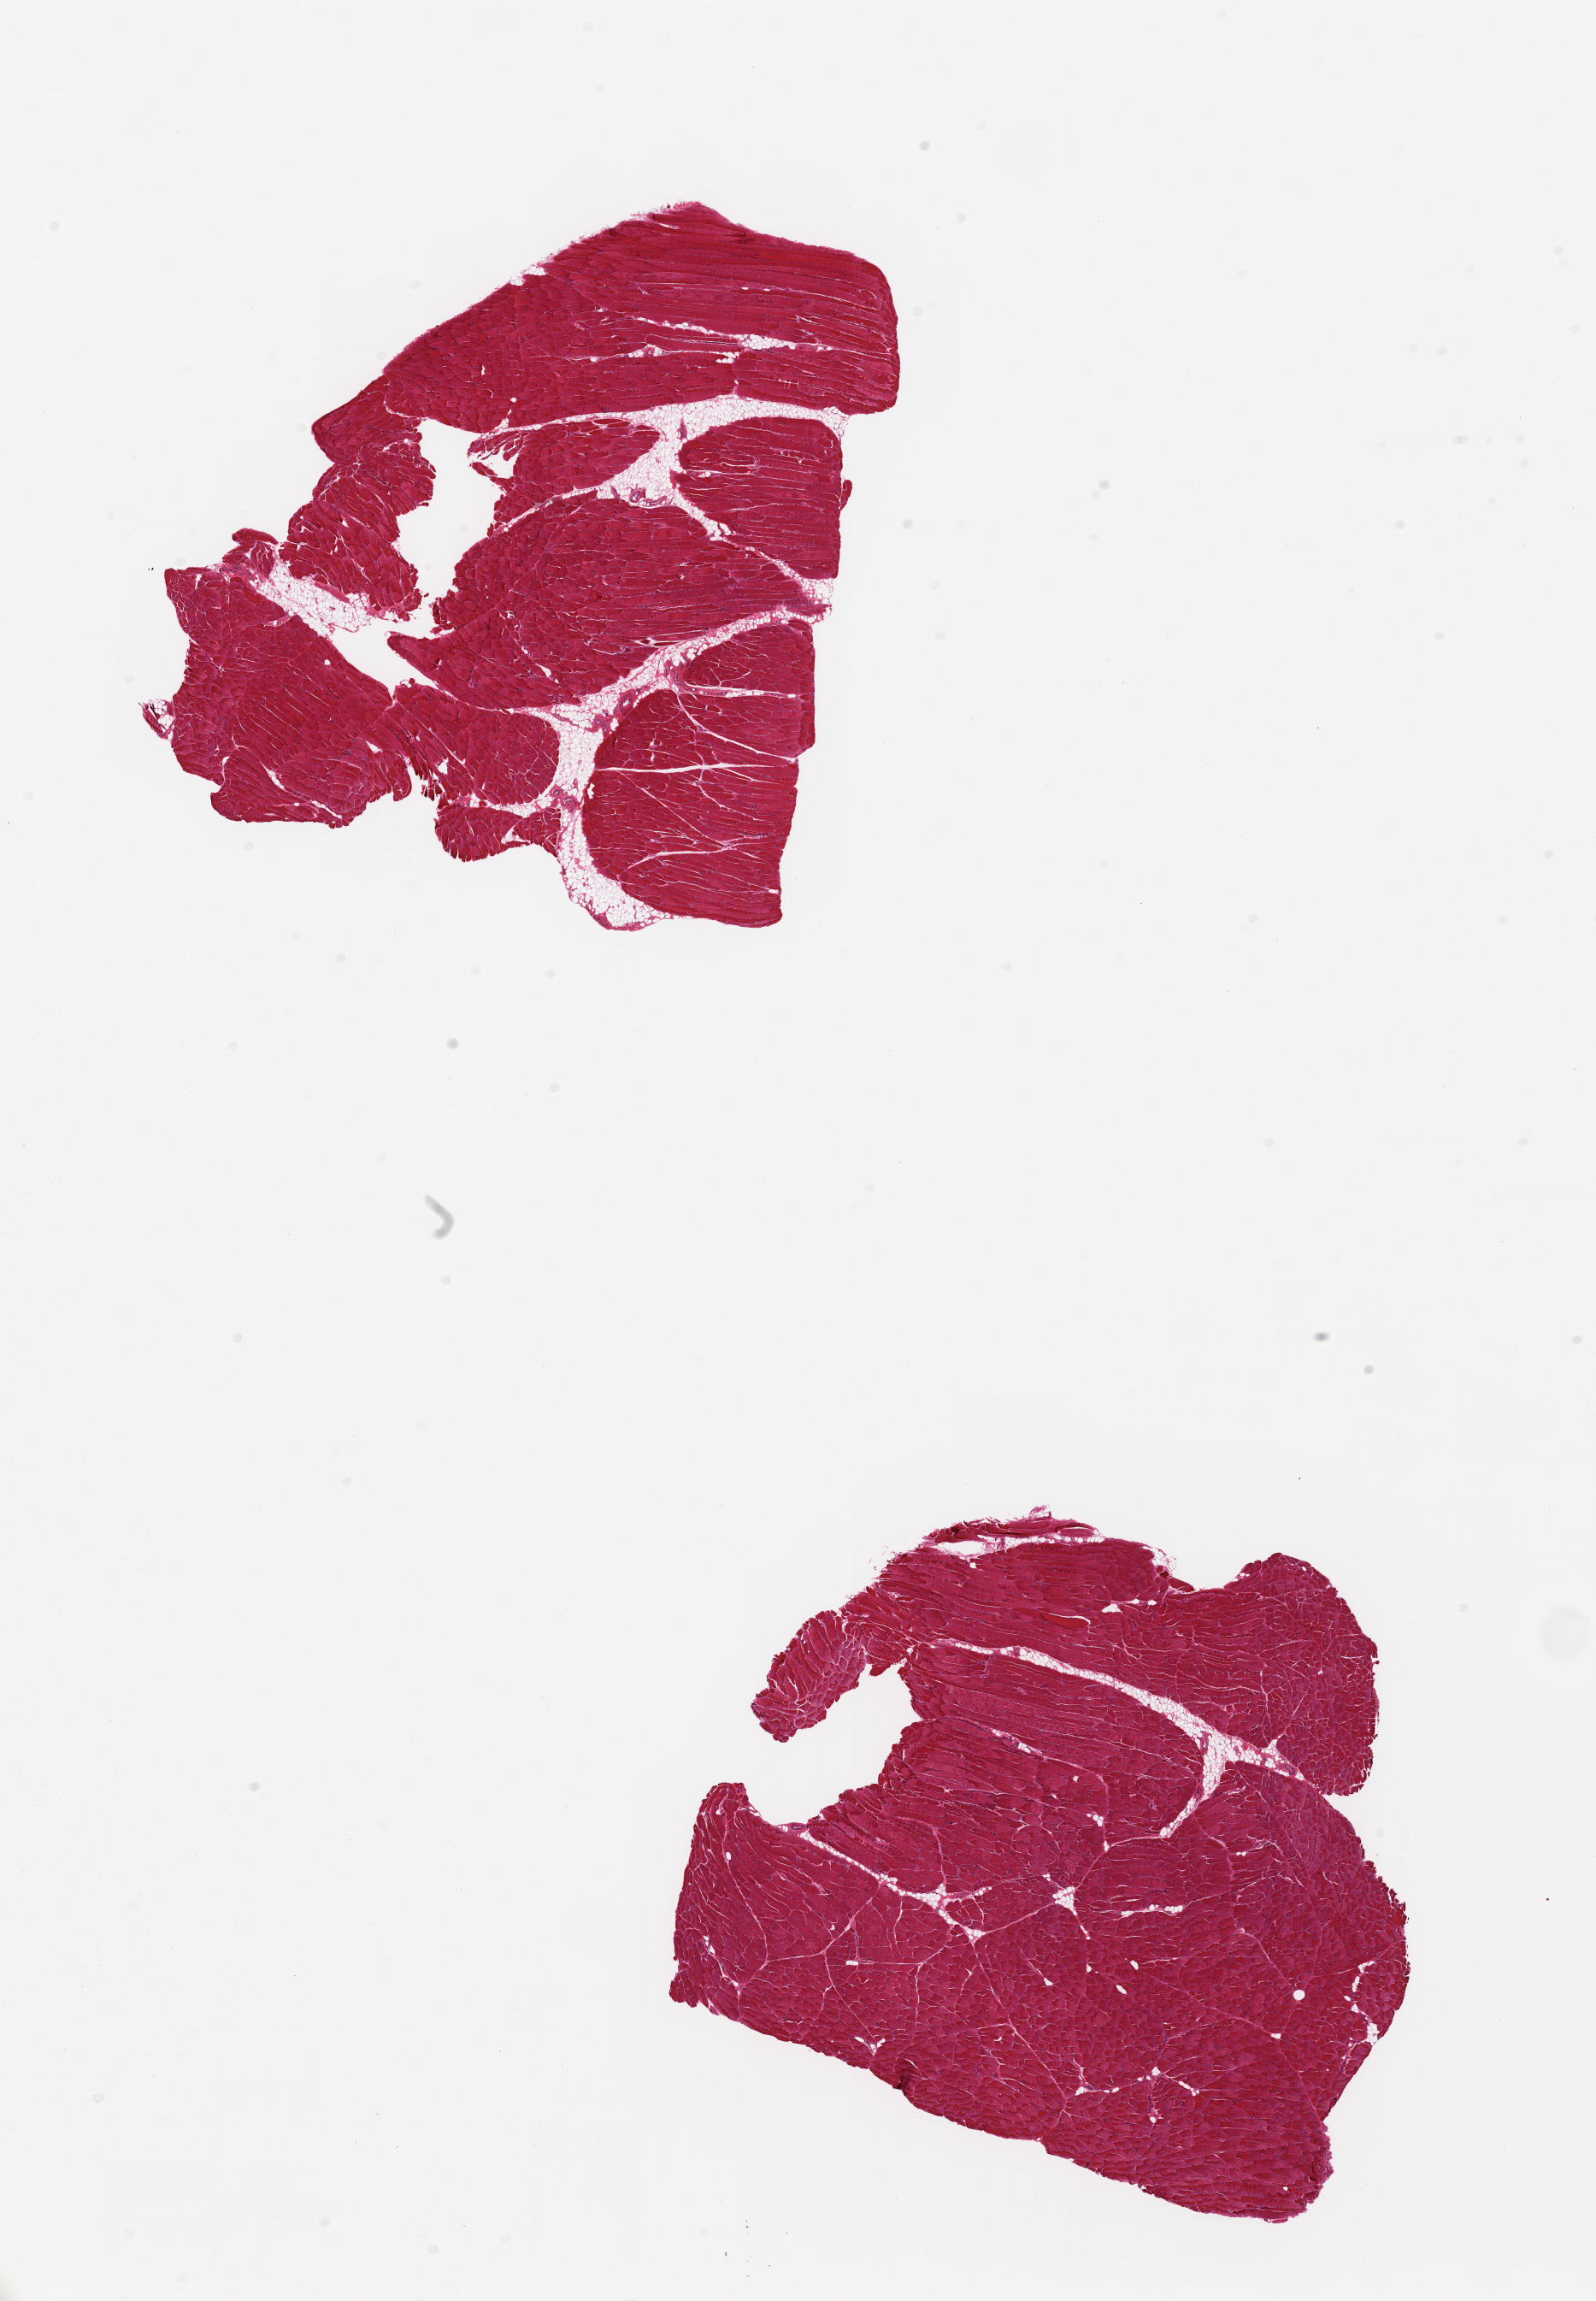
Digitized H&E-stained section — shown as a low-resolution overview of the whole scanned area (about 14.8 x 21.3 mm), PAXgene-fixed paraffin-embedded (PFPE) section, sampled site (target tissue): skeletal muscle, donor tissue sample. Donor: female.
* review note (as recorded): 2 pieces; 5% fat content